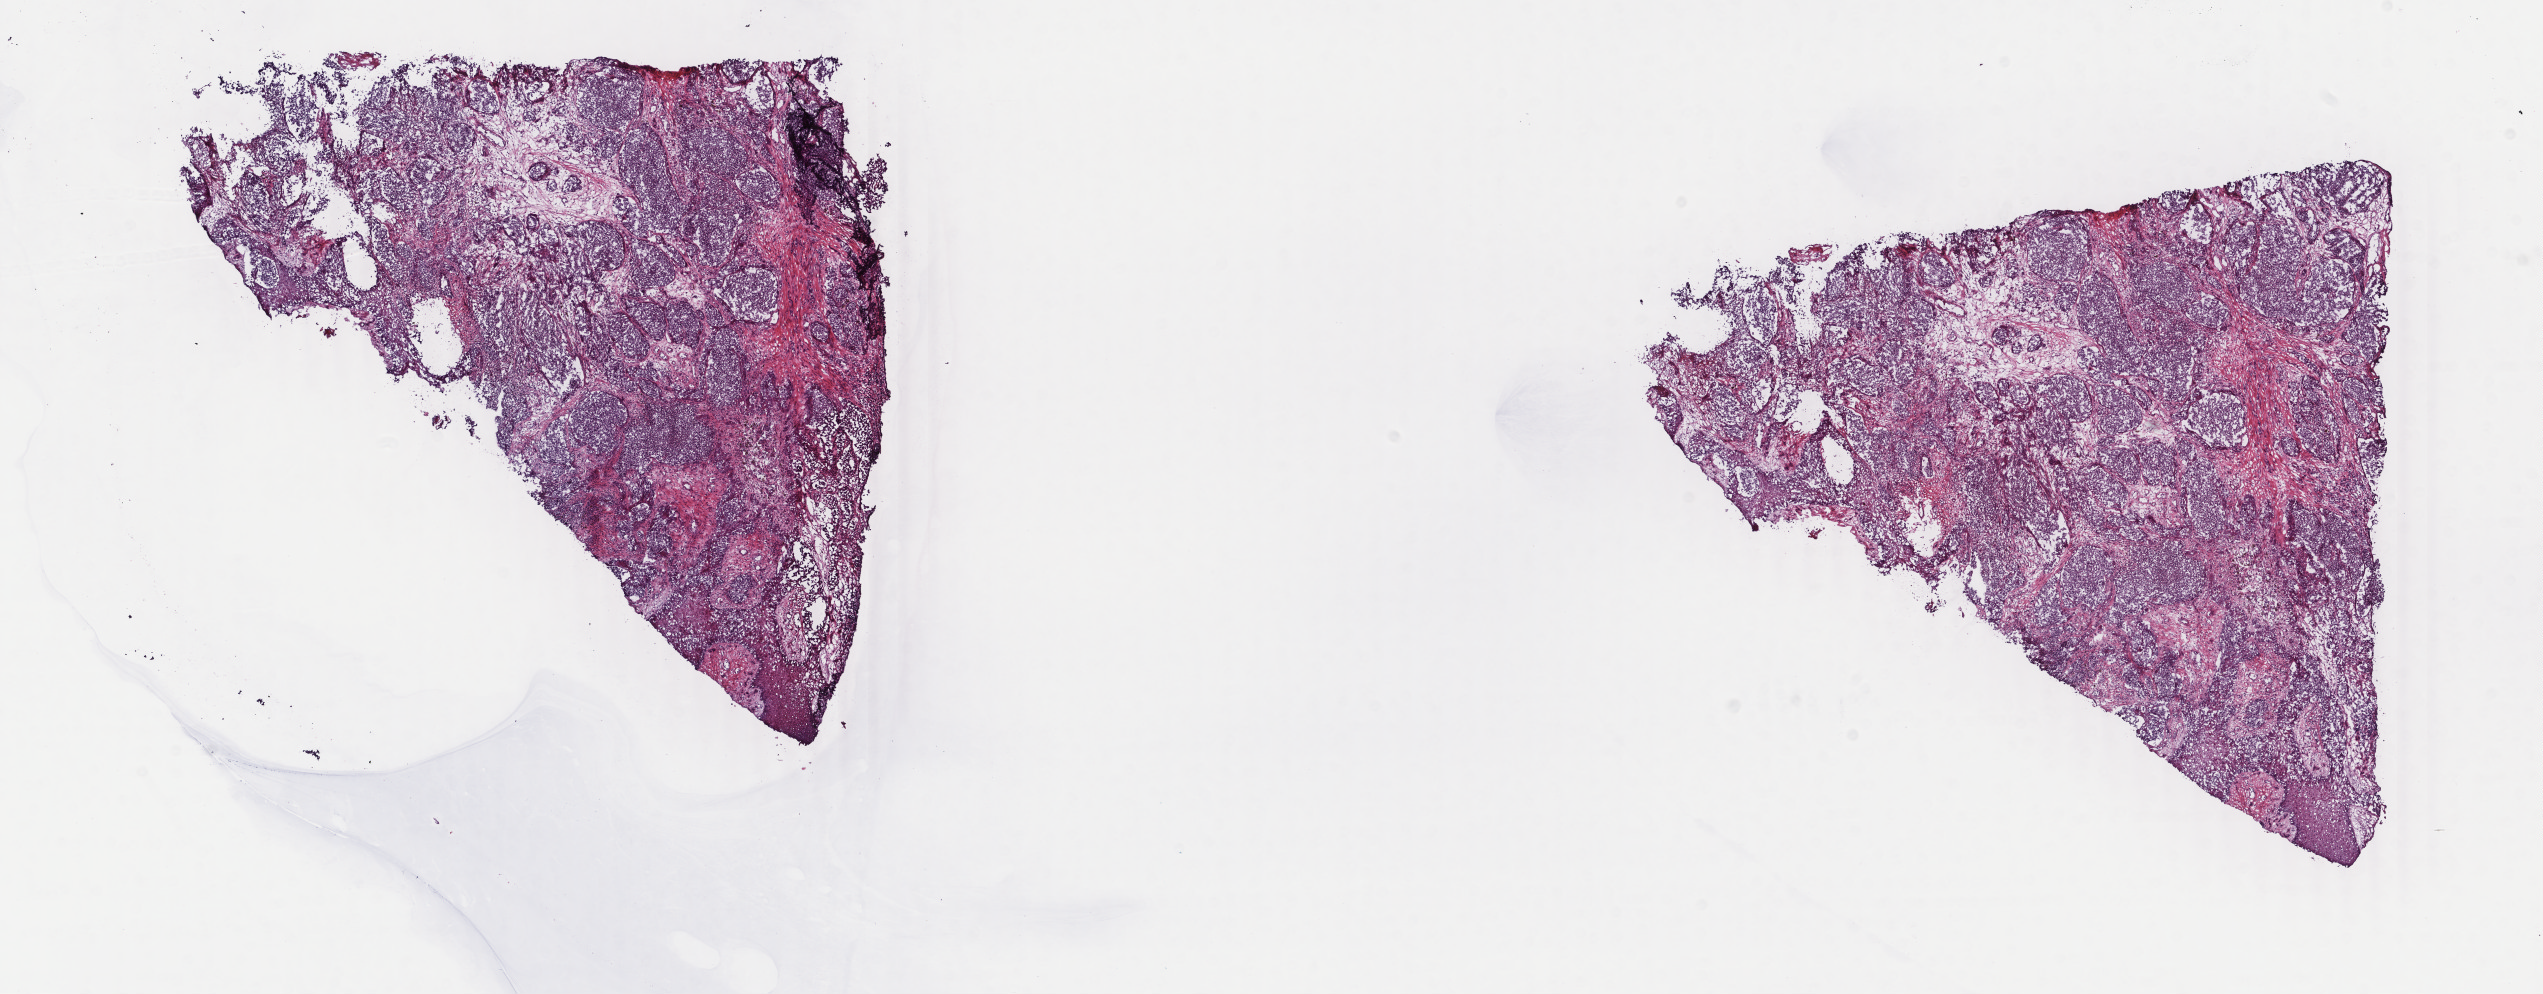
Hematoxylin and eosin (H&E) stained whole-slide image — shown as a low-resolution overview of the whole scanned area (about 20.2 x 7.9 mm, from a 40x scan). Frozen section from the top of the tissue portion. Skin, primary tumour sample. Female patient; age at initial diagnosis 64 years. Slide review estimates, as recorded: tumour cells 90%, tumour nuclei 85%, normal cells 5%, stromal cells 5%, necrosis 0%. Infiltration values recorded for this section: lymphocyte infiltration 0%, monocyte infiltration 0%, neutrophil infiltration 0%.
• diagnosis: Acral lentiginous melanoma, malignant
• AJCC pathologic stage: IIC